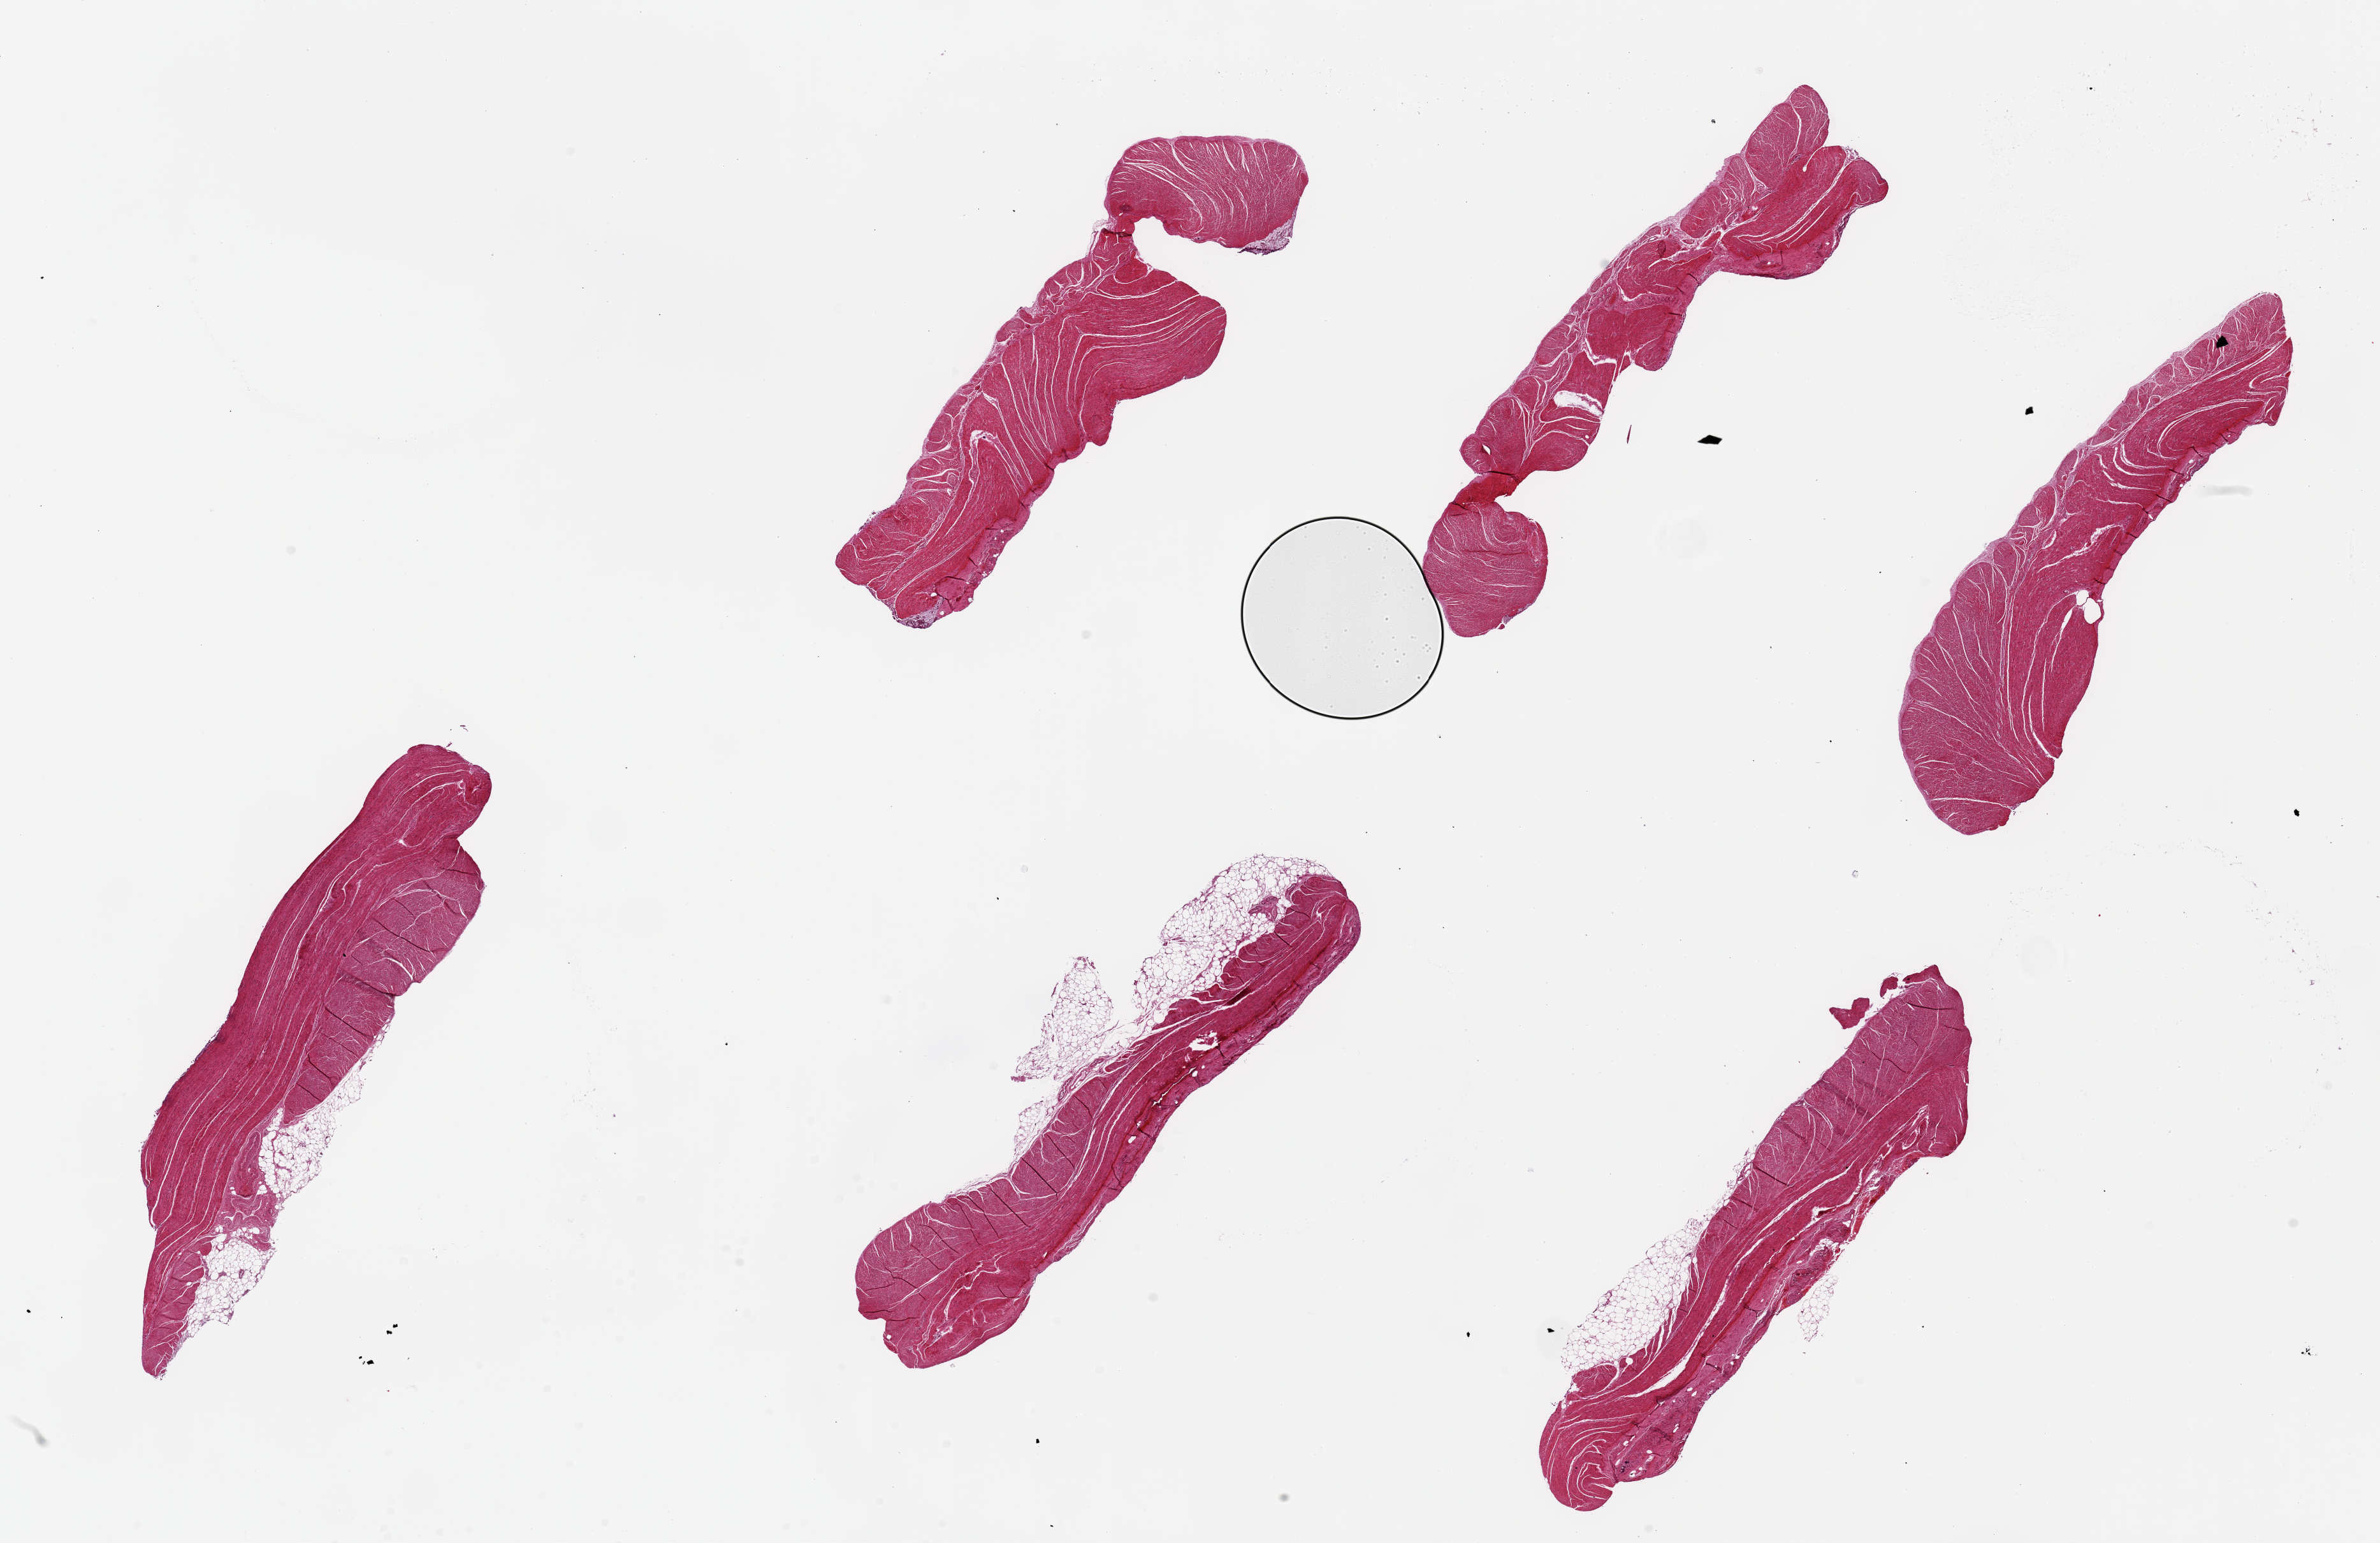
Whole-slide image, H&E stain — low-resolution overview of the scanned area, about 29.5 x 19.1 mm; PAXgene-fixed paraffin-embedded (PFPE) section; sampled site (target tissue): sigmoid colon; donor tissue sample. Male donor.
Review note (as recorded): 6 pieces, up to 9x2mm; All muscle (target). 3 pieces have up to 3x1 mm adipose on external surface.